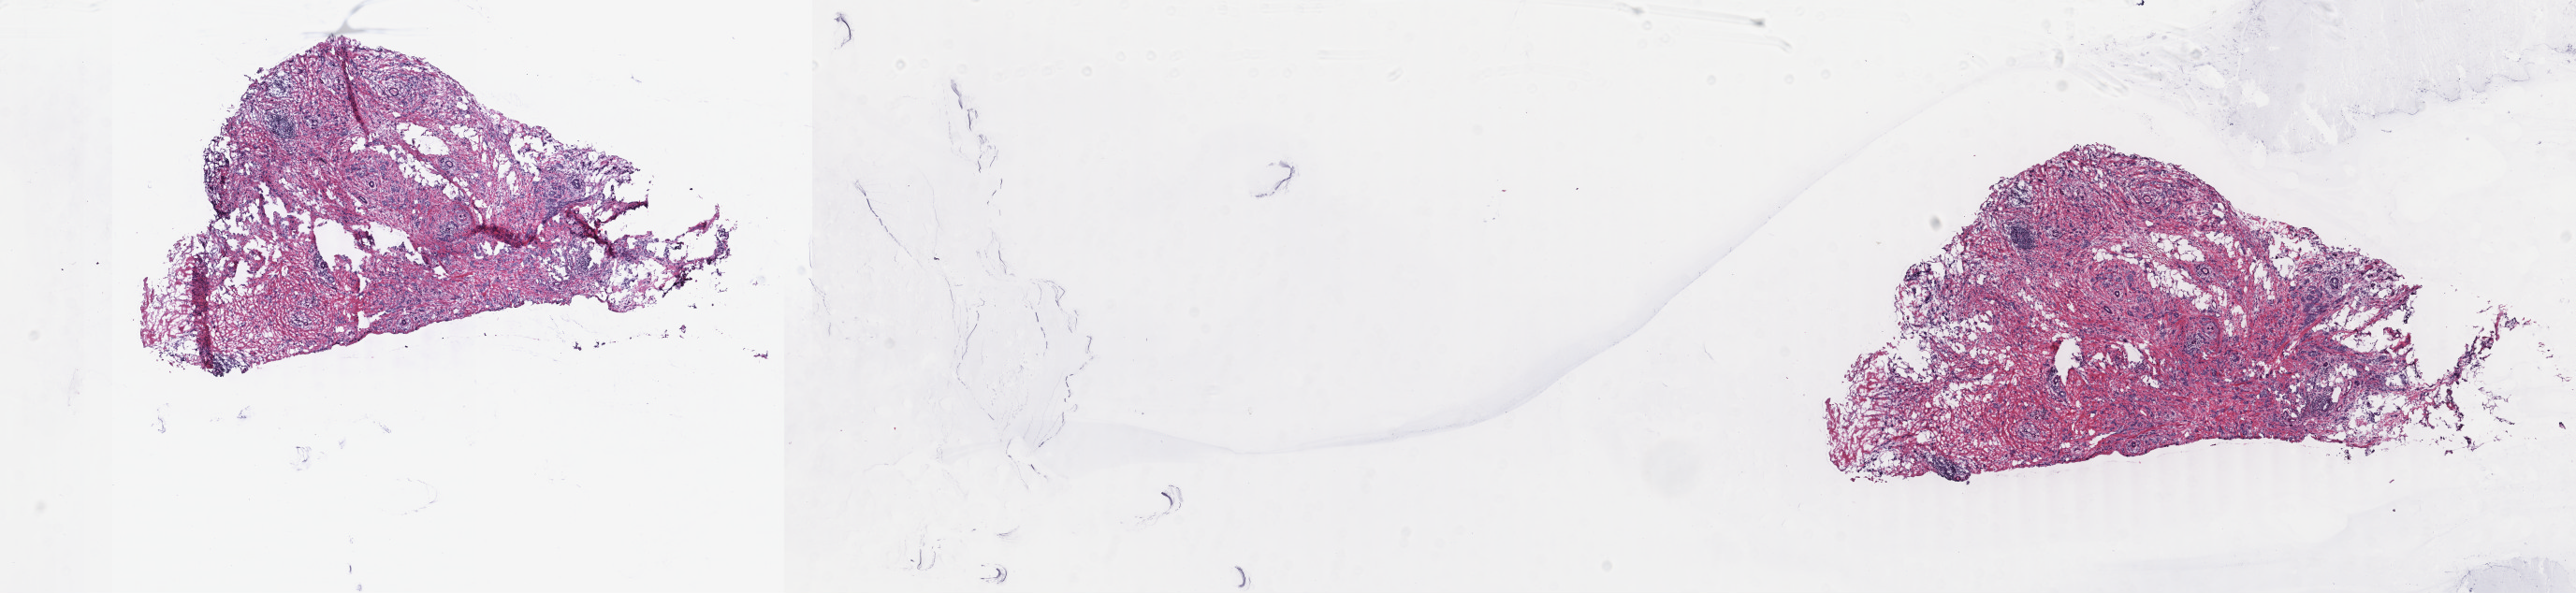
Digitized H&E-stained tissue section (whole slide) — whole scanned area (about 21.9 x 5.0 mm) shown as a low-resolution overview; frozen section from the top of the tissue portion; primary tumour sample from the breast. Female, age 80 years at initial diagnosis. Composition of this section per pathologist review: tumour cells 60%, tumour nuclei 75%, normal cells 10%, stromal cells 30%, necrosis 0%. Infiltration values recorded for this section: lymphocyte infiltration 0%, monocyte infiltration 0%, neutrophil infiltration 0%.
- lymph nodes positive (case pathology): 1 of 7 examined
- TNM: T1c N1a M0
- diagnosis: Infiltrating duct carcinoma, NOS
- AJCC pathologic stage: IIA (7th edition)